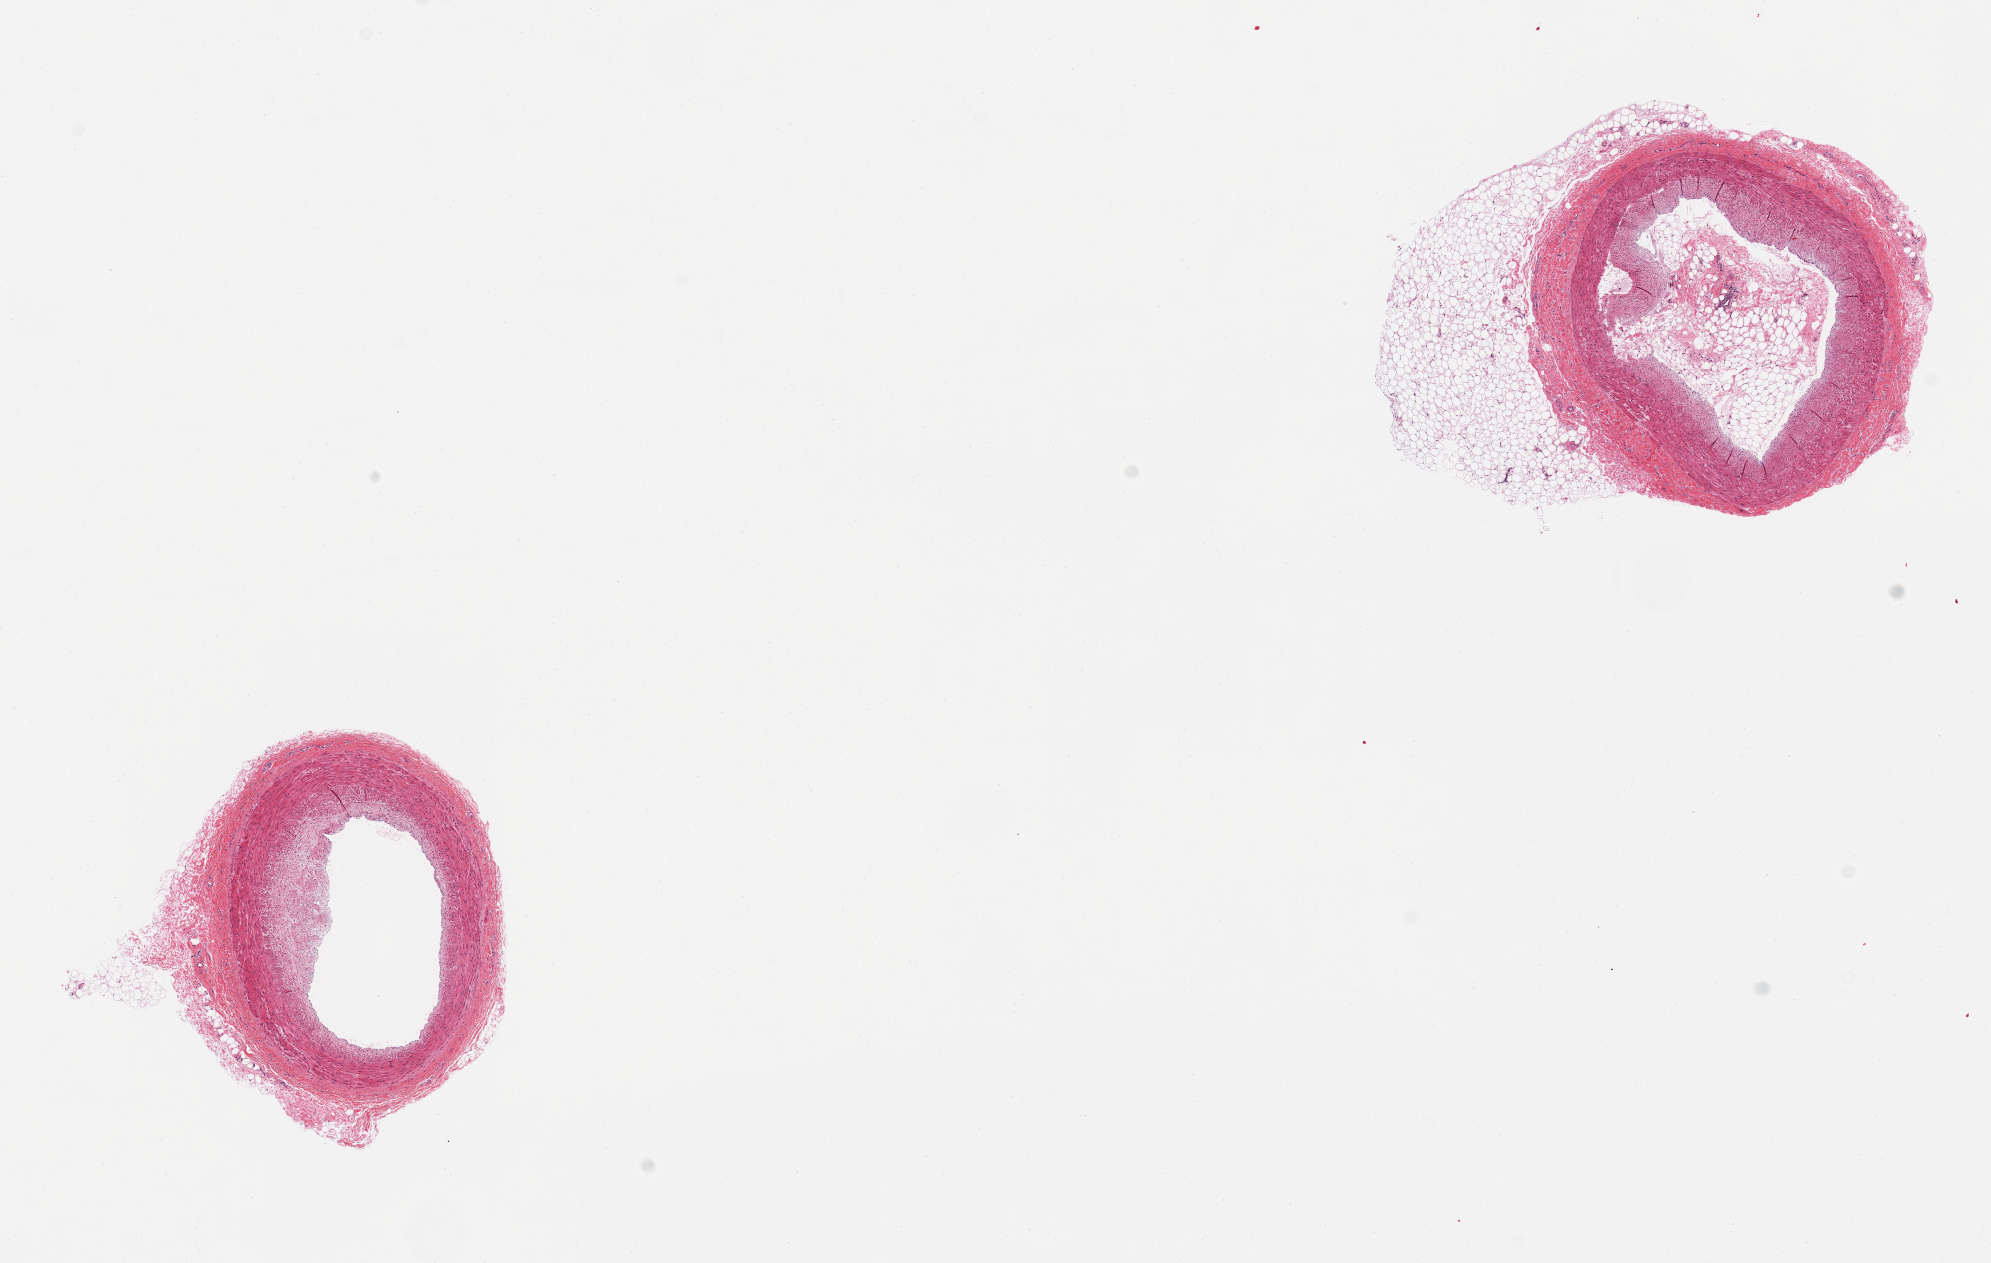
Whole-slide image, haematoxylin and eosin stain — shown as a low-resolution overview of the whole scanned area (about 15.8 x 10.0 mm); PAXgene-fixed paraffin-embedded (PFPE) section; section of coronary artery (target tissue); donor tissue sample. Donor: male.
Pathologist's review note for this sample: 2 pieces, one piece is 50% fat.